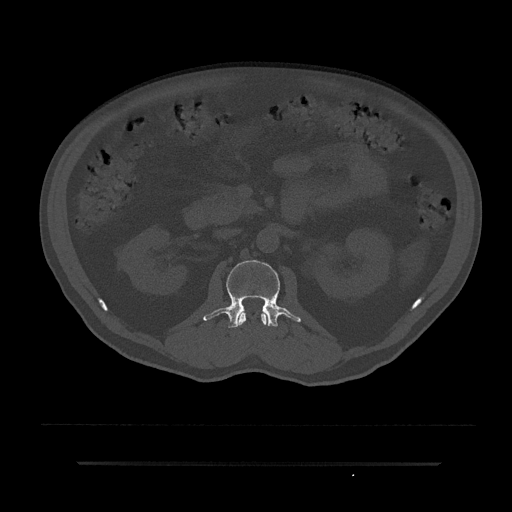
CT including the spine, one axial slice. Slice 92 of 797 in the series (ordered by position). Reconstruction kernel Br40s/3. 120 kVp. Bone window (W 1800 / L 400 HU). 0.5 mm slice thickness. 512 × 512 image matrix, field of view 464 × 464 mm. Patient: male, 59 years. From the clinical record (not read from this slice): primary cancer: bile ducts.
Structures marked on this image (semi-automatic segmentation, software-assisted and operator-edited):
- L1 vertebra: bounding box (x1, y1, x2, y2) in pixels: (238, 311, 267, 326)
- L2 vertebra: (203, 260, 301, 328)